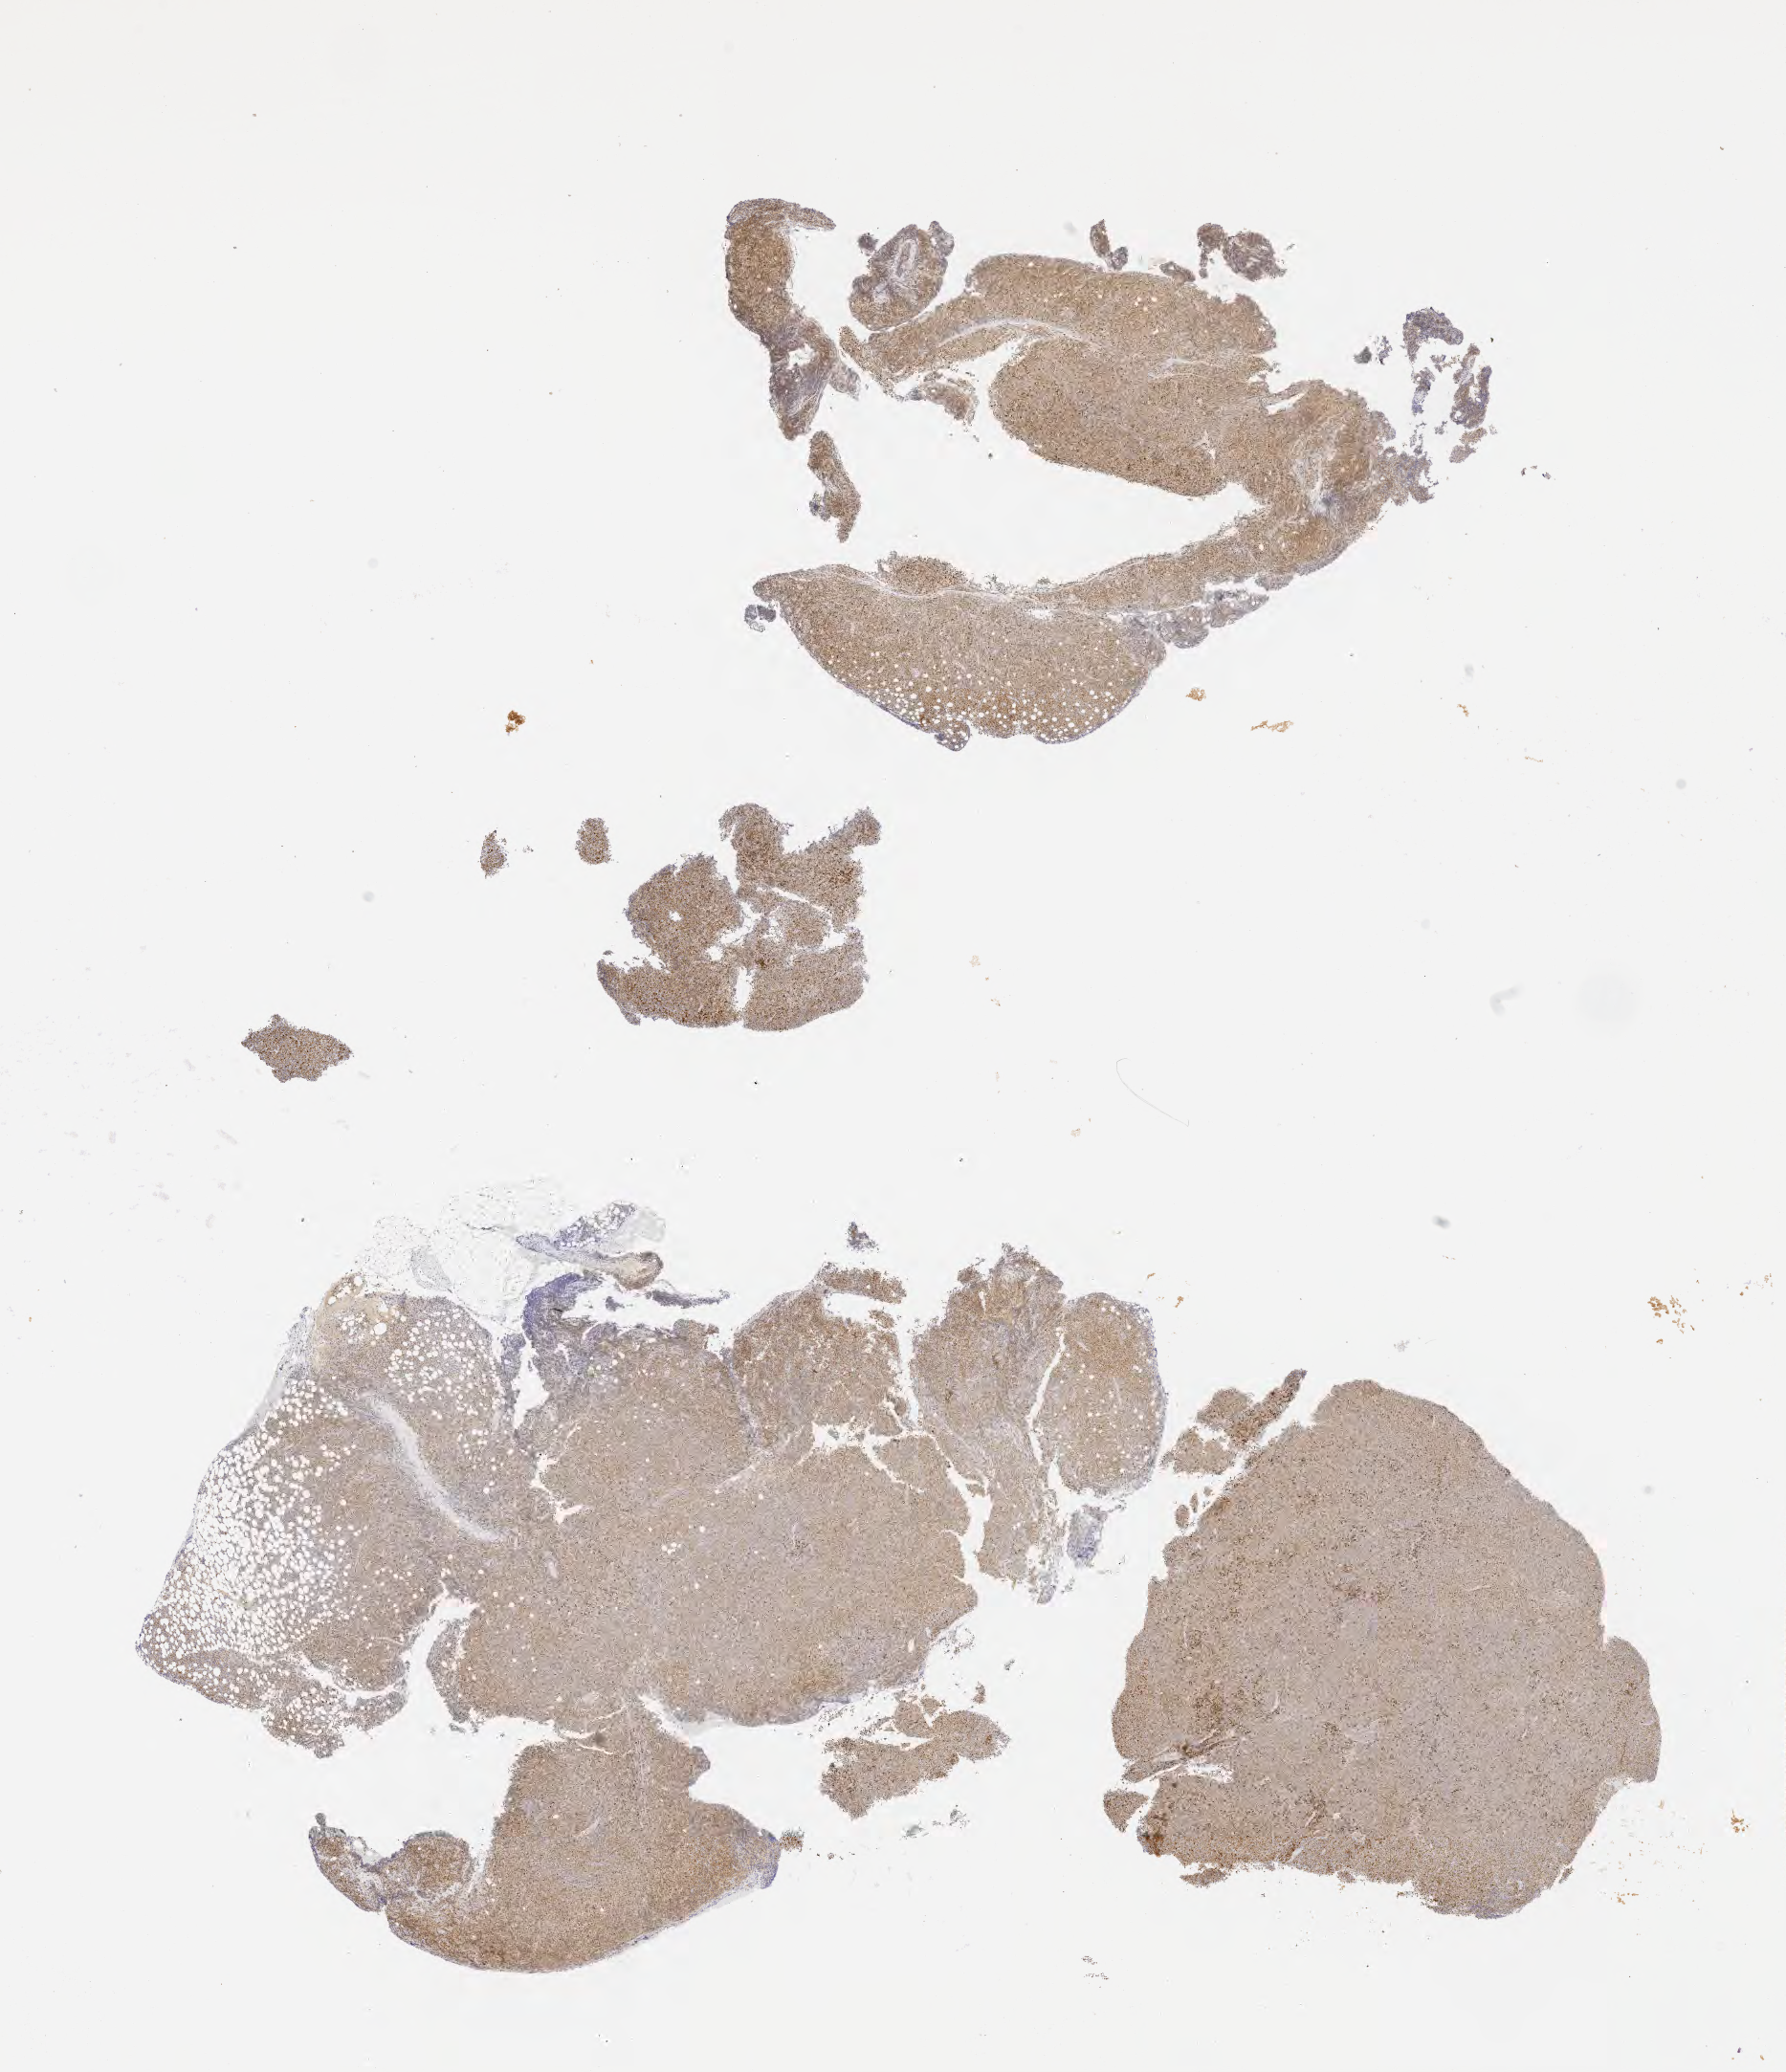
Whole-slide image, immunohistochemical stain for IRF4/MUM1 — low-resolution overview of the scanned area, about 15.1 x 17.5 mm. Specimen: tumor tissue. Patient female; aged 32.
* histologic diagnosis: Diffuse large B-cell lymphoma, NOS